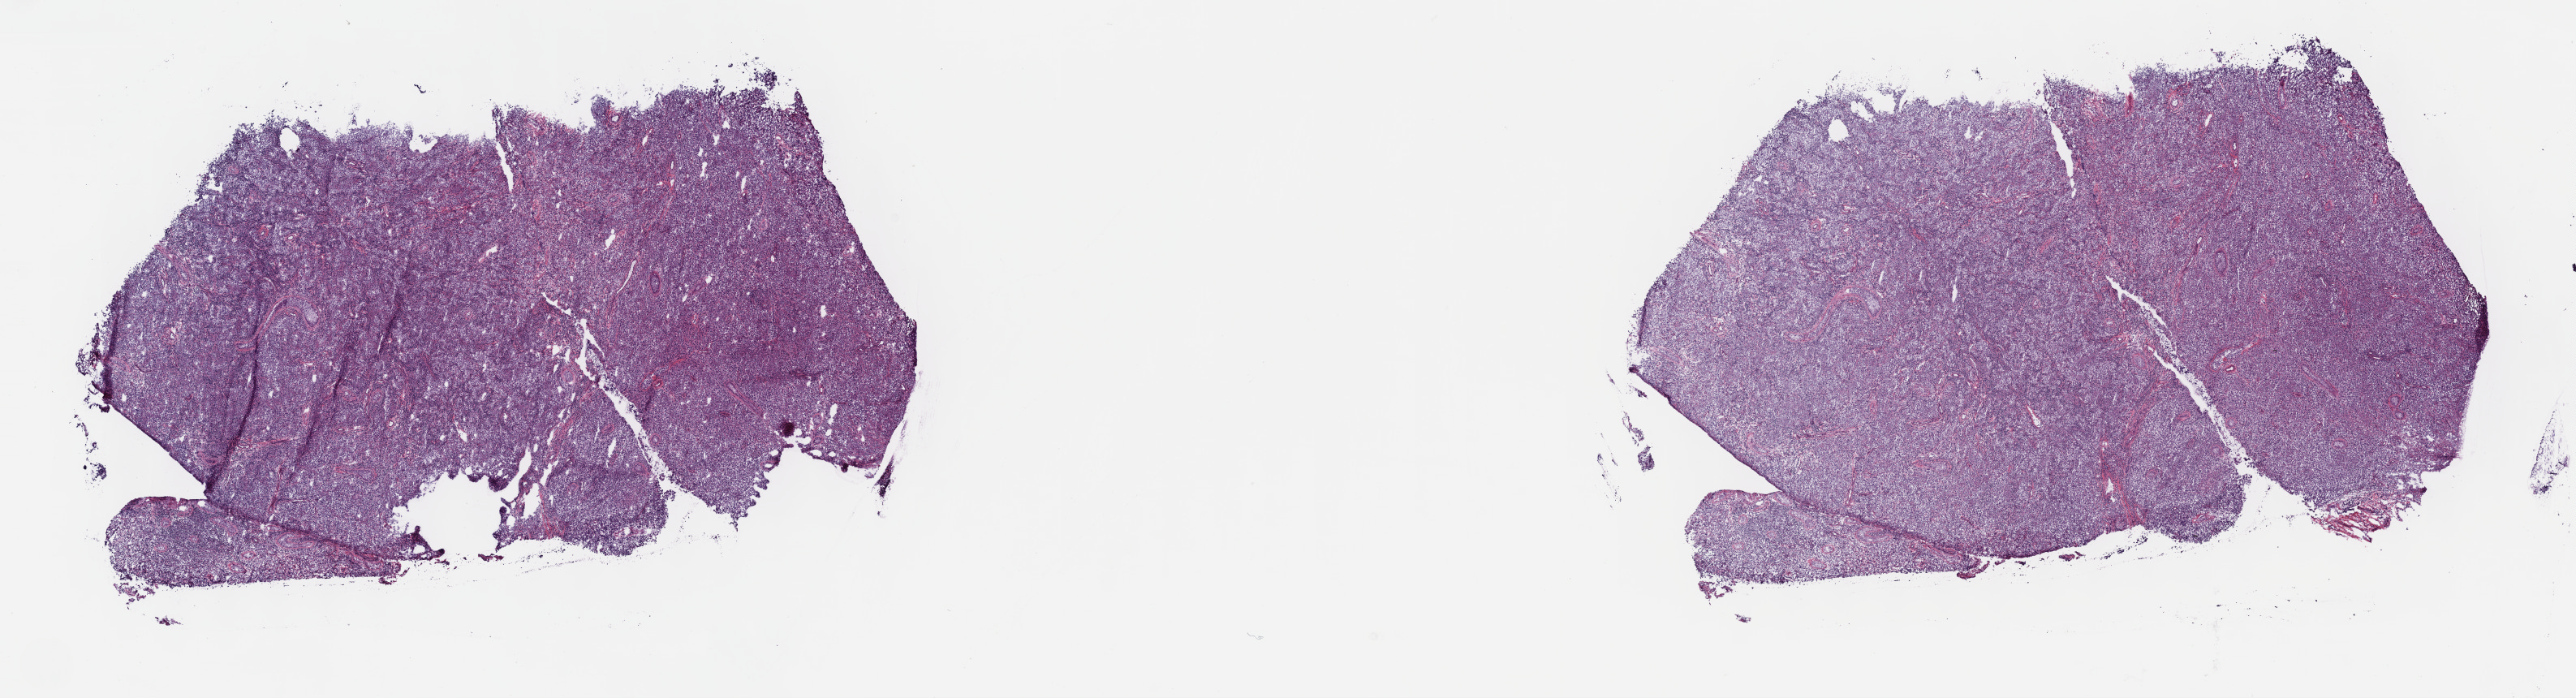
Digitized H&E tissue section (whole slide), whole scanned area (about 25.7 x 7.0 mm, from a 40x scan) shown as a low-resolution overview, frozen section from the top of the tissue portion, sample: primary tumour, testis. Patient: male, age at initial diagnosis 32 years. Slide review estimates, as recorded: tumour cells 90%, tumour nuclei 90%, normal cells 0%, stromal cells 10%, necrosis 0%. Inflammatory infiltration, as recorded: lymphocyte infiltration 40%, monocyte infiltration 20%, neutrophil infiltration 20%.
• laterality: left
• diagnosis: Seminoma, NOS
• TNM: T1 N0 M0
• AJCC pathologic stage: I (4th edition)